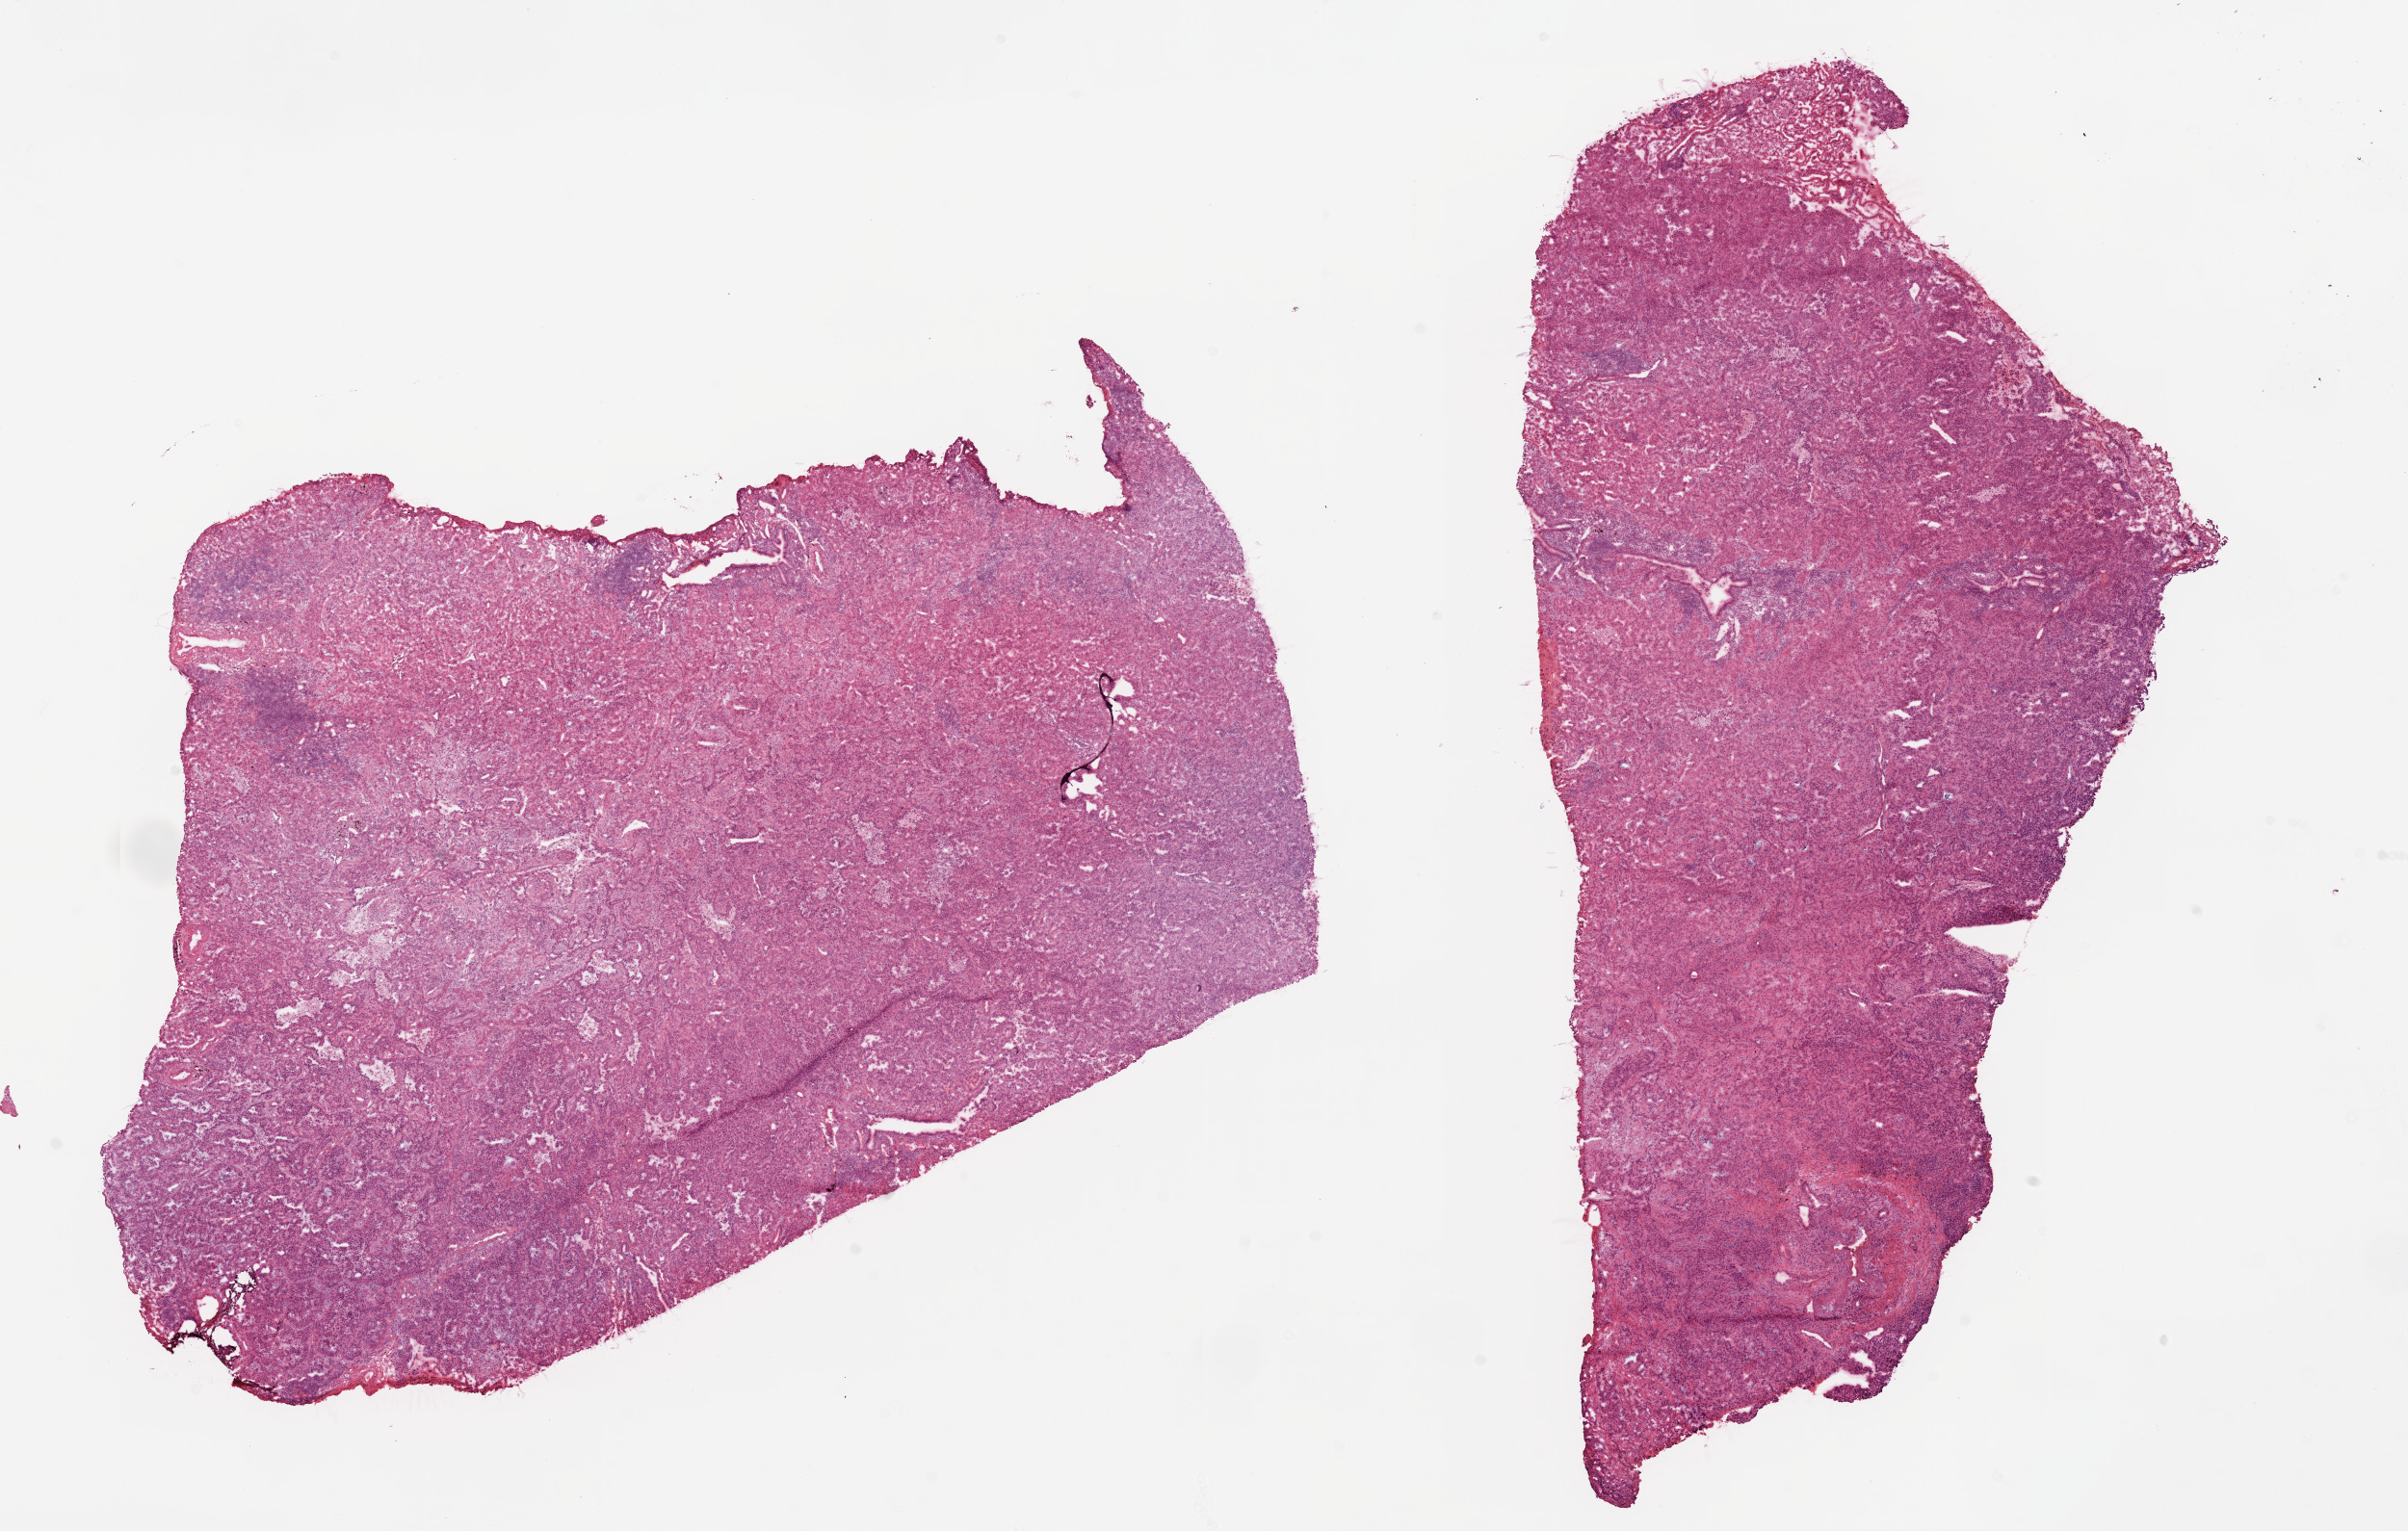
H&E whole-slide image, a low-resolution overview of the entire scanned area, about 20.1 x 12.8 mm. Frozen section from the top of the tissue portion. Primary tumour sample from the lung. Female, age 74 years at initial diagnosis. Composition of this section per pathologist review: tumour cells 83%, tumour nuclei 60%, normal cells 2%, stromal cells 15%, necrosis 0%.
AJCC pathologic stage: IA (3rd edition). Diagnosis: Adenocarcinoma, NOS (lower lobe, lung).